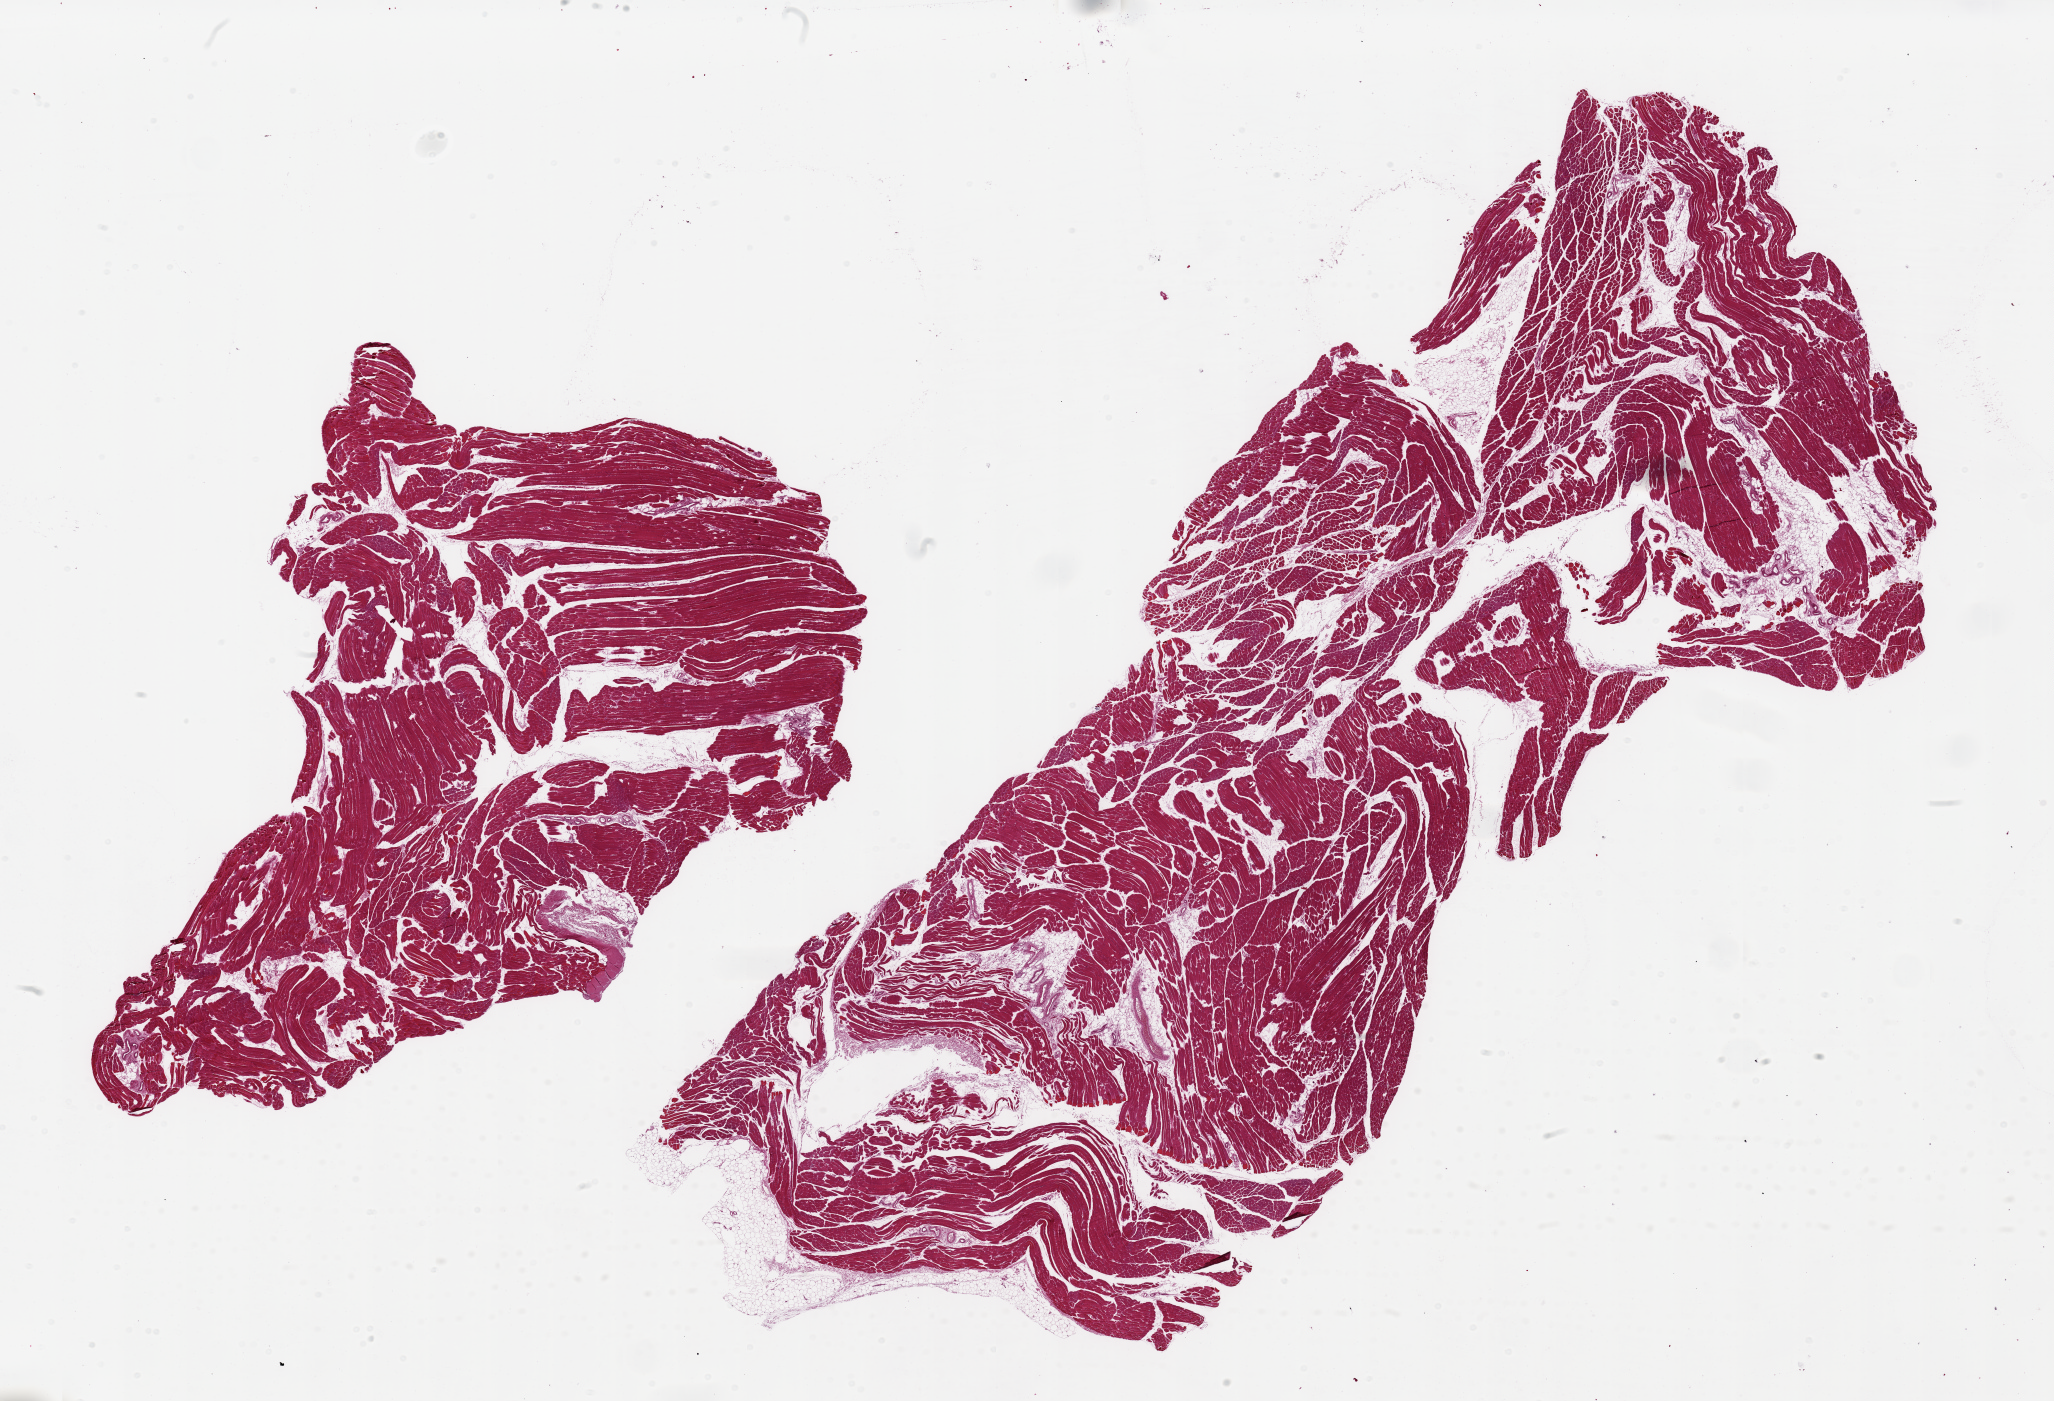
Hematoxylin and eosin (H&E) whole-slide image, brightfield — a low-resolution overview of the entire scanned area, about 32.5 x 22.2 mm; PAXgene-fixed, paraffin-embedded tissue; section of skeletal muscle (target tissue); donor tissue sample. Donor: female.
* reviewer comment on this tissue sample: 2 pieces, 15x10 & 24.5x10mm; 10--20% interstitialfat